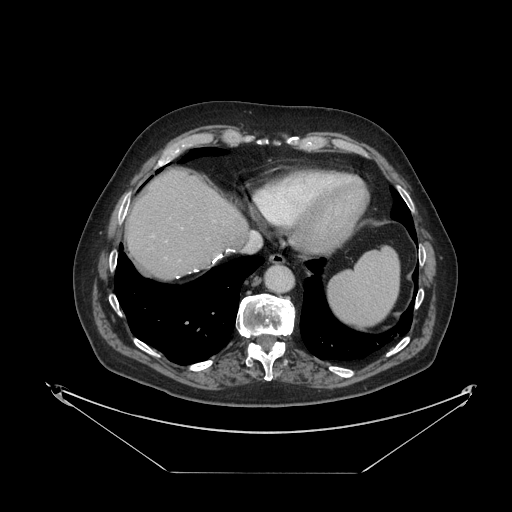
Contrast-enhanced abdominal CT, one axial slice; position 105 of 121 along the scan axis; 120 kVp; intravenous contrast given; soft-tissue window (W 400 / L 40 HU); 2.5 mm slice thickness; 512 × 512 image matrix, field of view 500 × 500 mm. Male patient, age 68 years. Case-level facts recorded for this patient, not image findings: diagnosis: colorectal cancer liver metastases, imaged before liver resection; multiple liver metastases: no; largest metastasis: 4 cm; disease in both lobes: no.
Outlined on this slice (outlined manually by an expert reader):
- liver: bounding box (x1, y1, x2, y2) in pixels: (127, 171, 248, 278)
- planned liver remnant (the part of the liver to remain after resection): (127, 171, 248, 278)